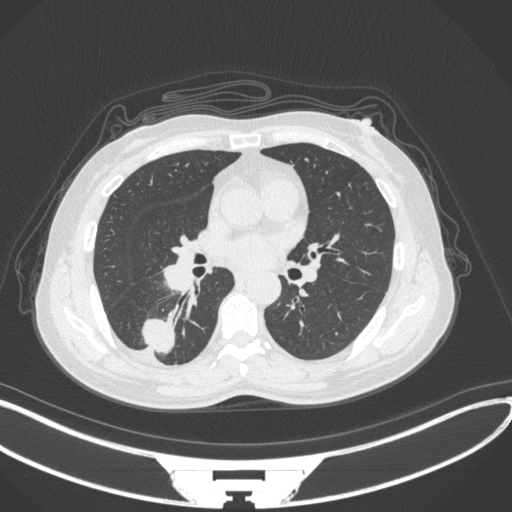
Chest CT, one axial slice; slice 156 of 352 in the series (ordered by position); reconstruction kernel B31f; lung window (W 1500 / L -600 HU); 1 mm slice thickness; 512 × 512 image matrix, field of view 400 × 400 mm. Female patient, age 55 years. From the clinical record (not read from this slice): clinical TNM (as recorded): T1c N1 M0.
Outlined on this slice (rectangle marked by the reading radiologist):
- lung tumour (recorded histology: adenocarcinoma): bounding box (x1, y1, x2, y2) in pixels: (137, 314, 182, 355)